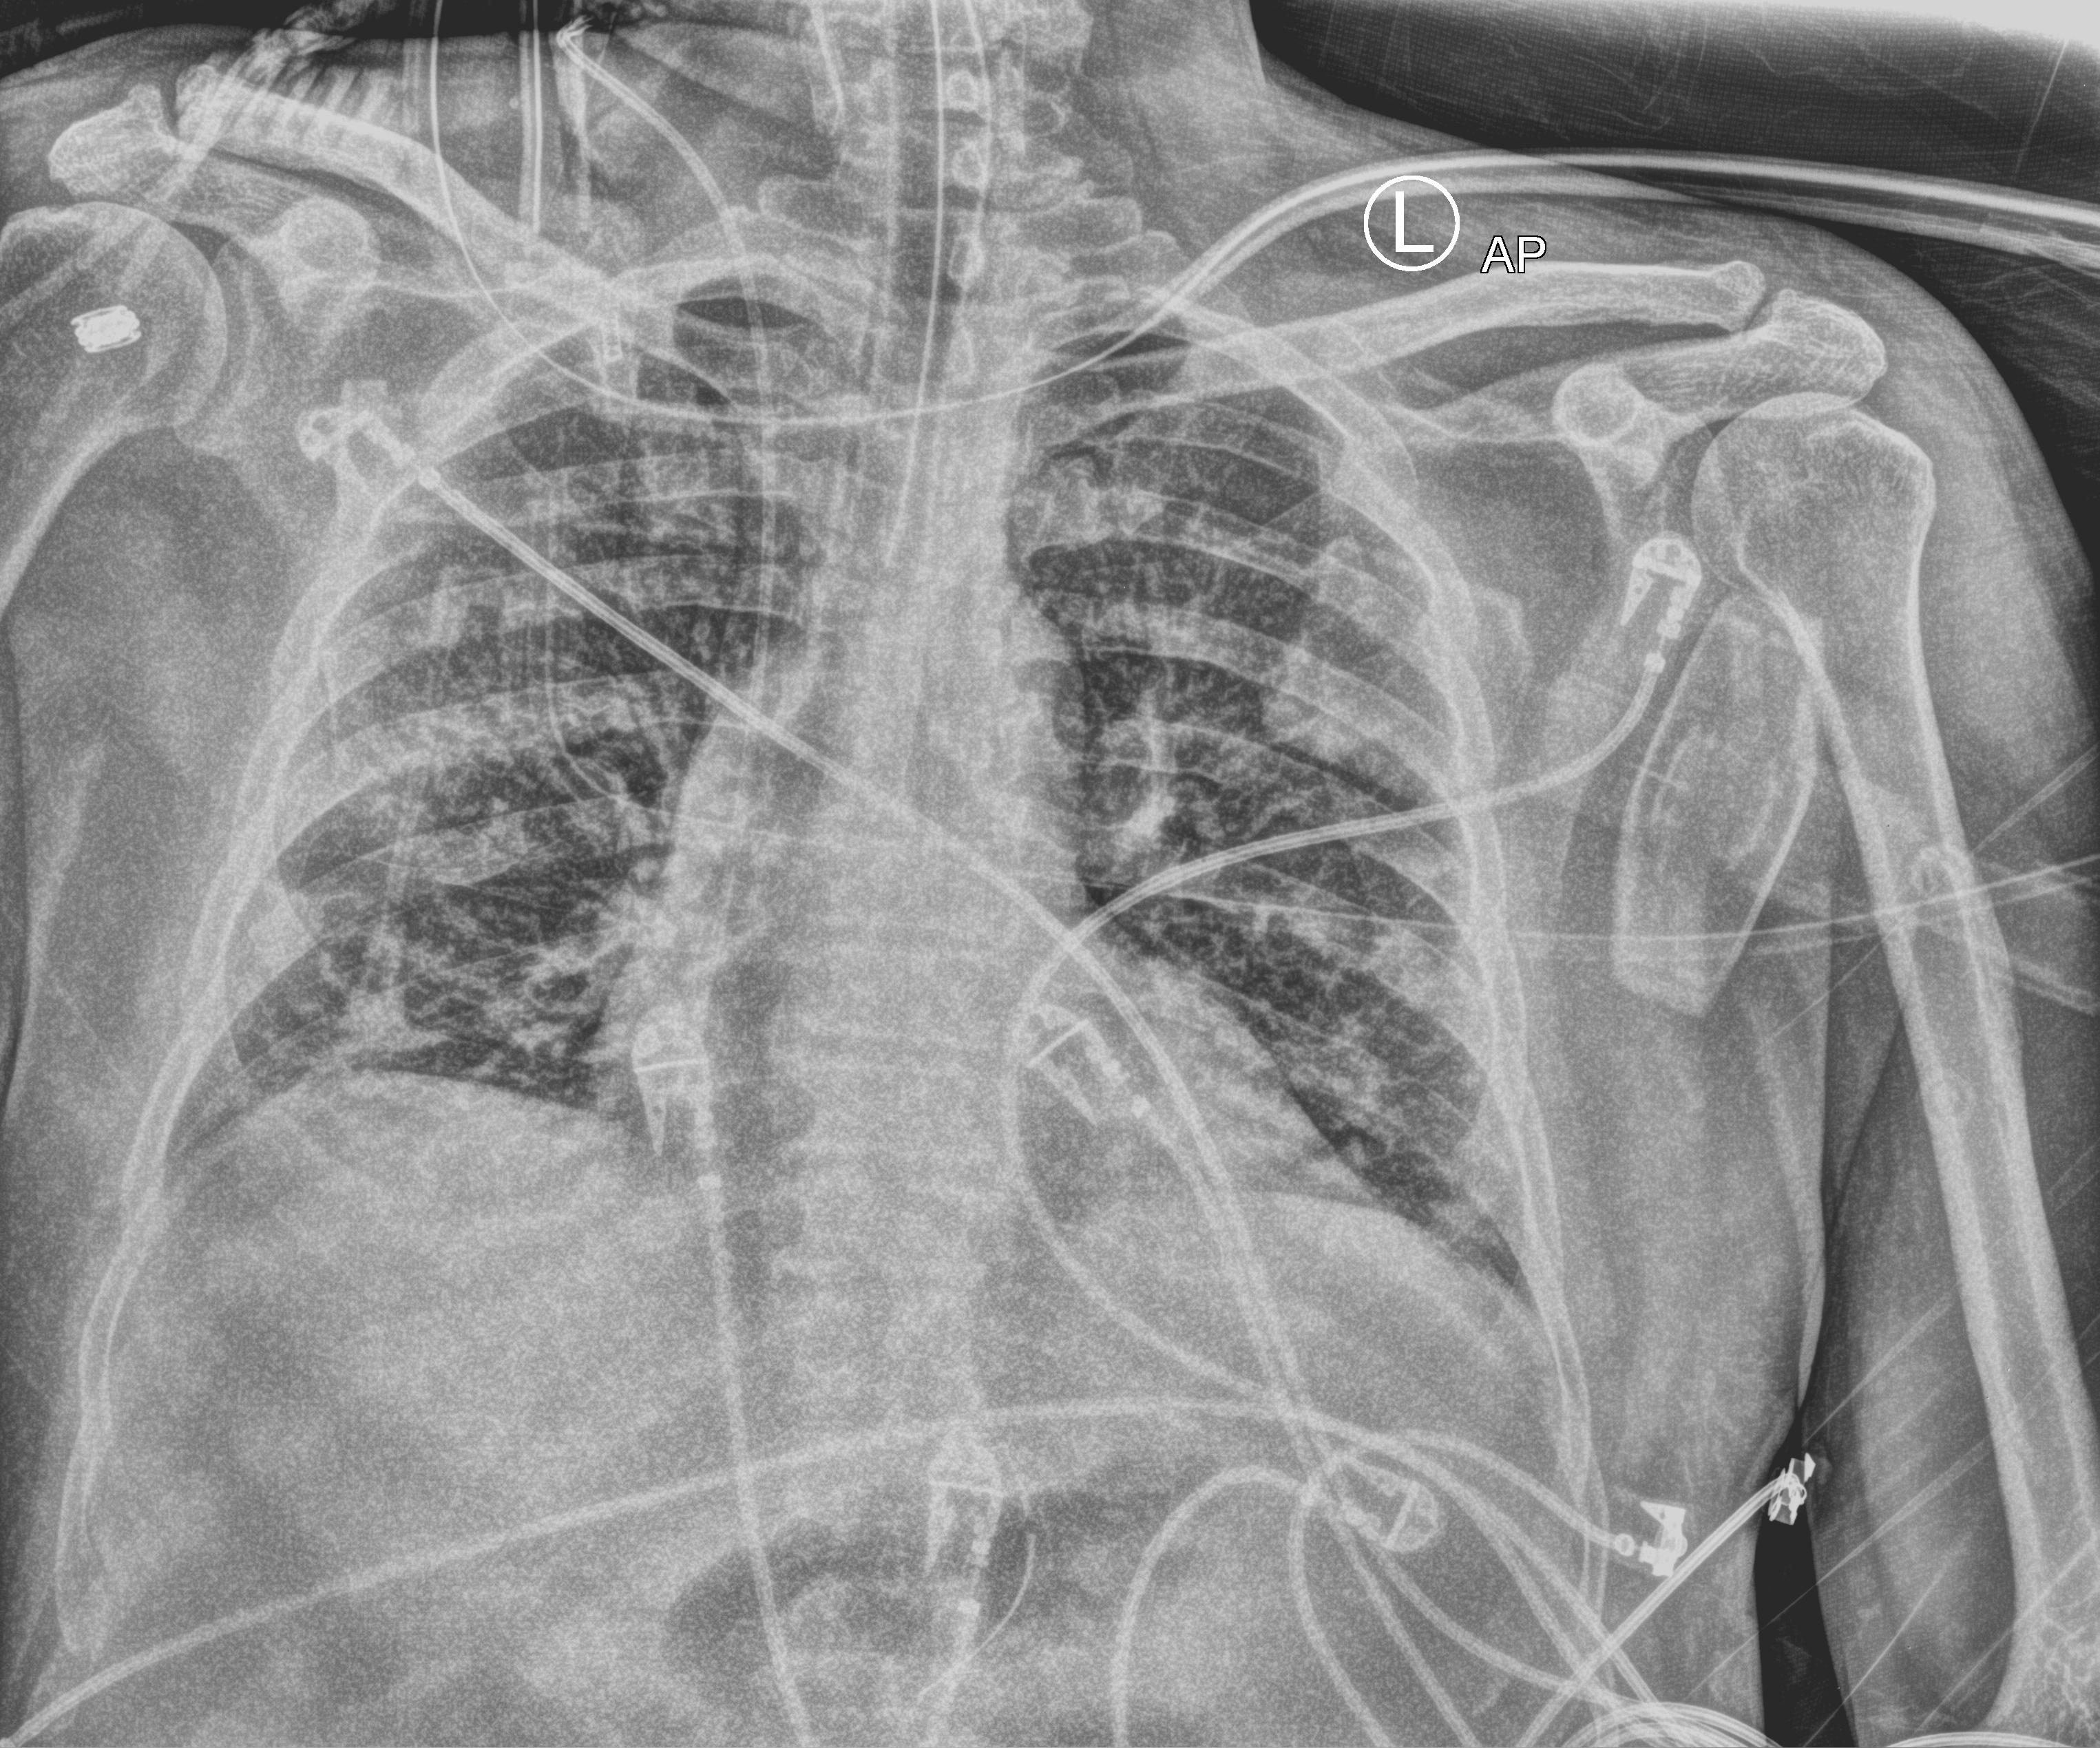
Chest X-ray (portable), anteroposterior (AP) projection. Patient hospitalised with COVID-19; male, aged 18–59 years.
Hospital-stay facts (about this admission, not read from this image; timing relative to this image not recorded): mechanically ventilated during this hospital stay: yes; chronic kidney disease (admission record): no.